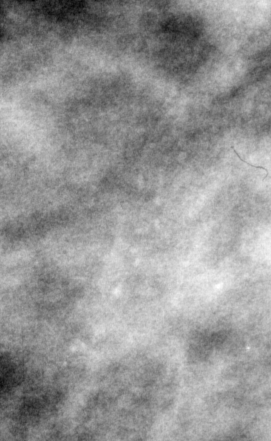
Region of interest cut from a scanned film mammogram (one marked finding); left breast; MLO view.
Marked abnormality: calcifications, morphology pleomorphic, distribution clustered; BI-RADS assessment category 4; pathology result (as recorded, not read from the image): malignant.